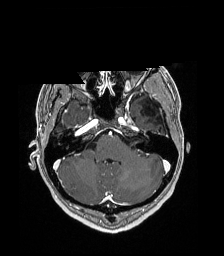
Brain MRI from a brain-tumour surgery series, one axial slice. Position 135 of 192 along the scan axis. T1-weighted post-contrast. 1 mm slice thickness. 224 × 256 image matrix, field of view 224 × 256 mm. From the clinical record (not read from this slice): histopathology: Low grade glioma; IDH mutation: no.
Outlined on this slice (expert manual segmentation):
- previous resection cavity: bounding box [x1, y1, x2, y2] px = [143, 103, 160, 116]